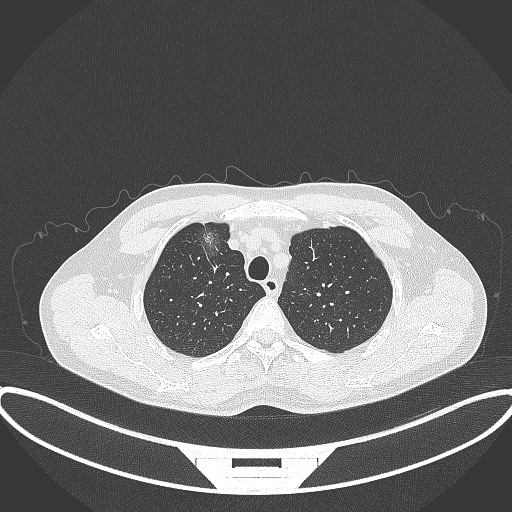
Chest CT, one axial slice; position 296 of 395 along the scan axis; reconstruction kernel B70f; lung window (W 1500 / L -600 HU); 512 × 512 image matrix, field of view 424 × 424 mm. Male patient, age 60 years. From the clinical record (not read from this slice): clinical TNM (as recorded): T1c N0 M0.
Structures marked on this image (rectangle marked by the reading radiologist):
- lung tumour (recorded histology: adenocarcinoma): bounding box (x1, y1, x2, y2) in pixels: (192, 217, 230, 260)